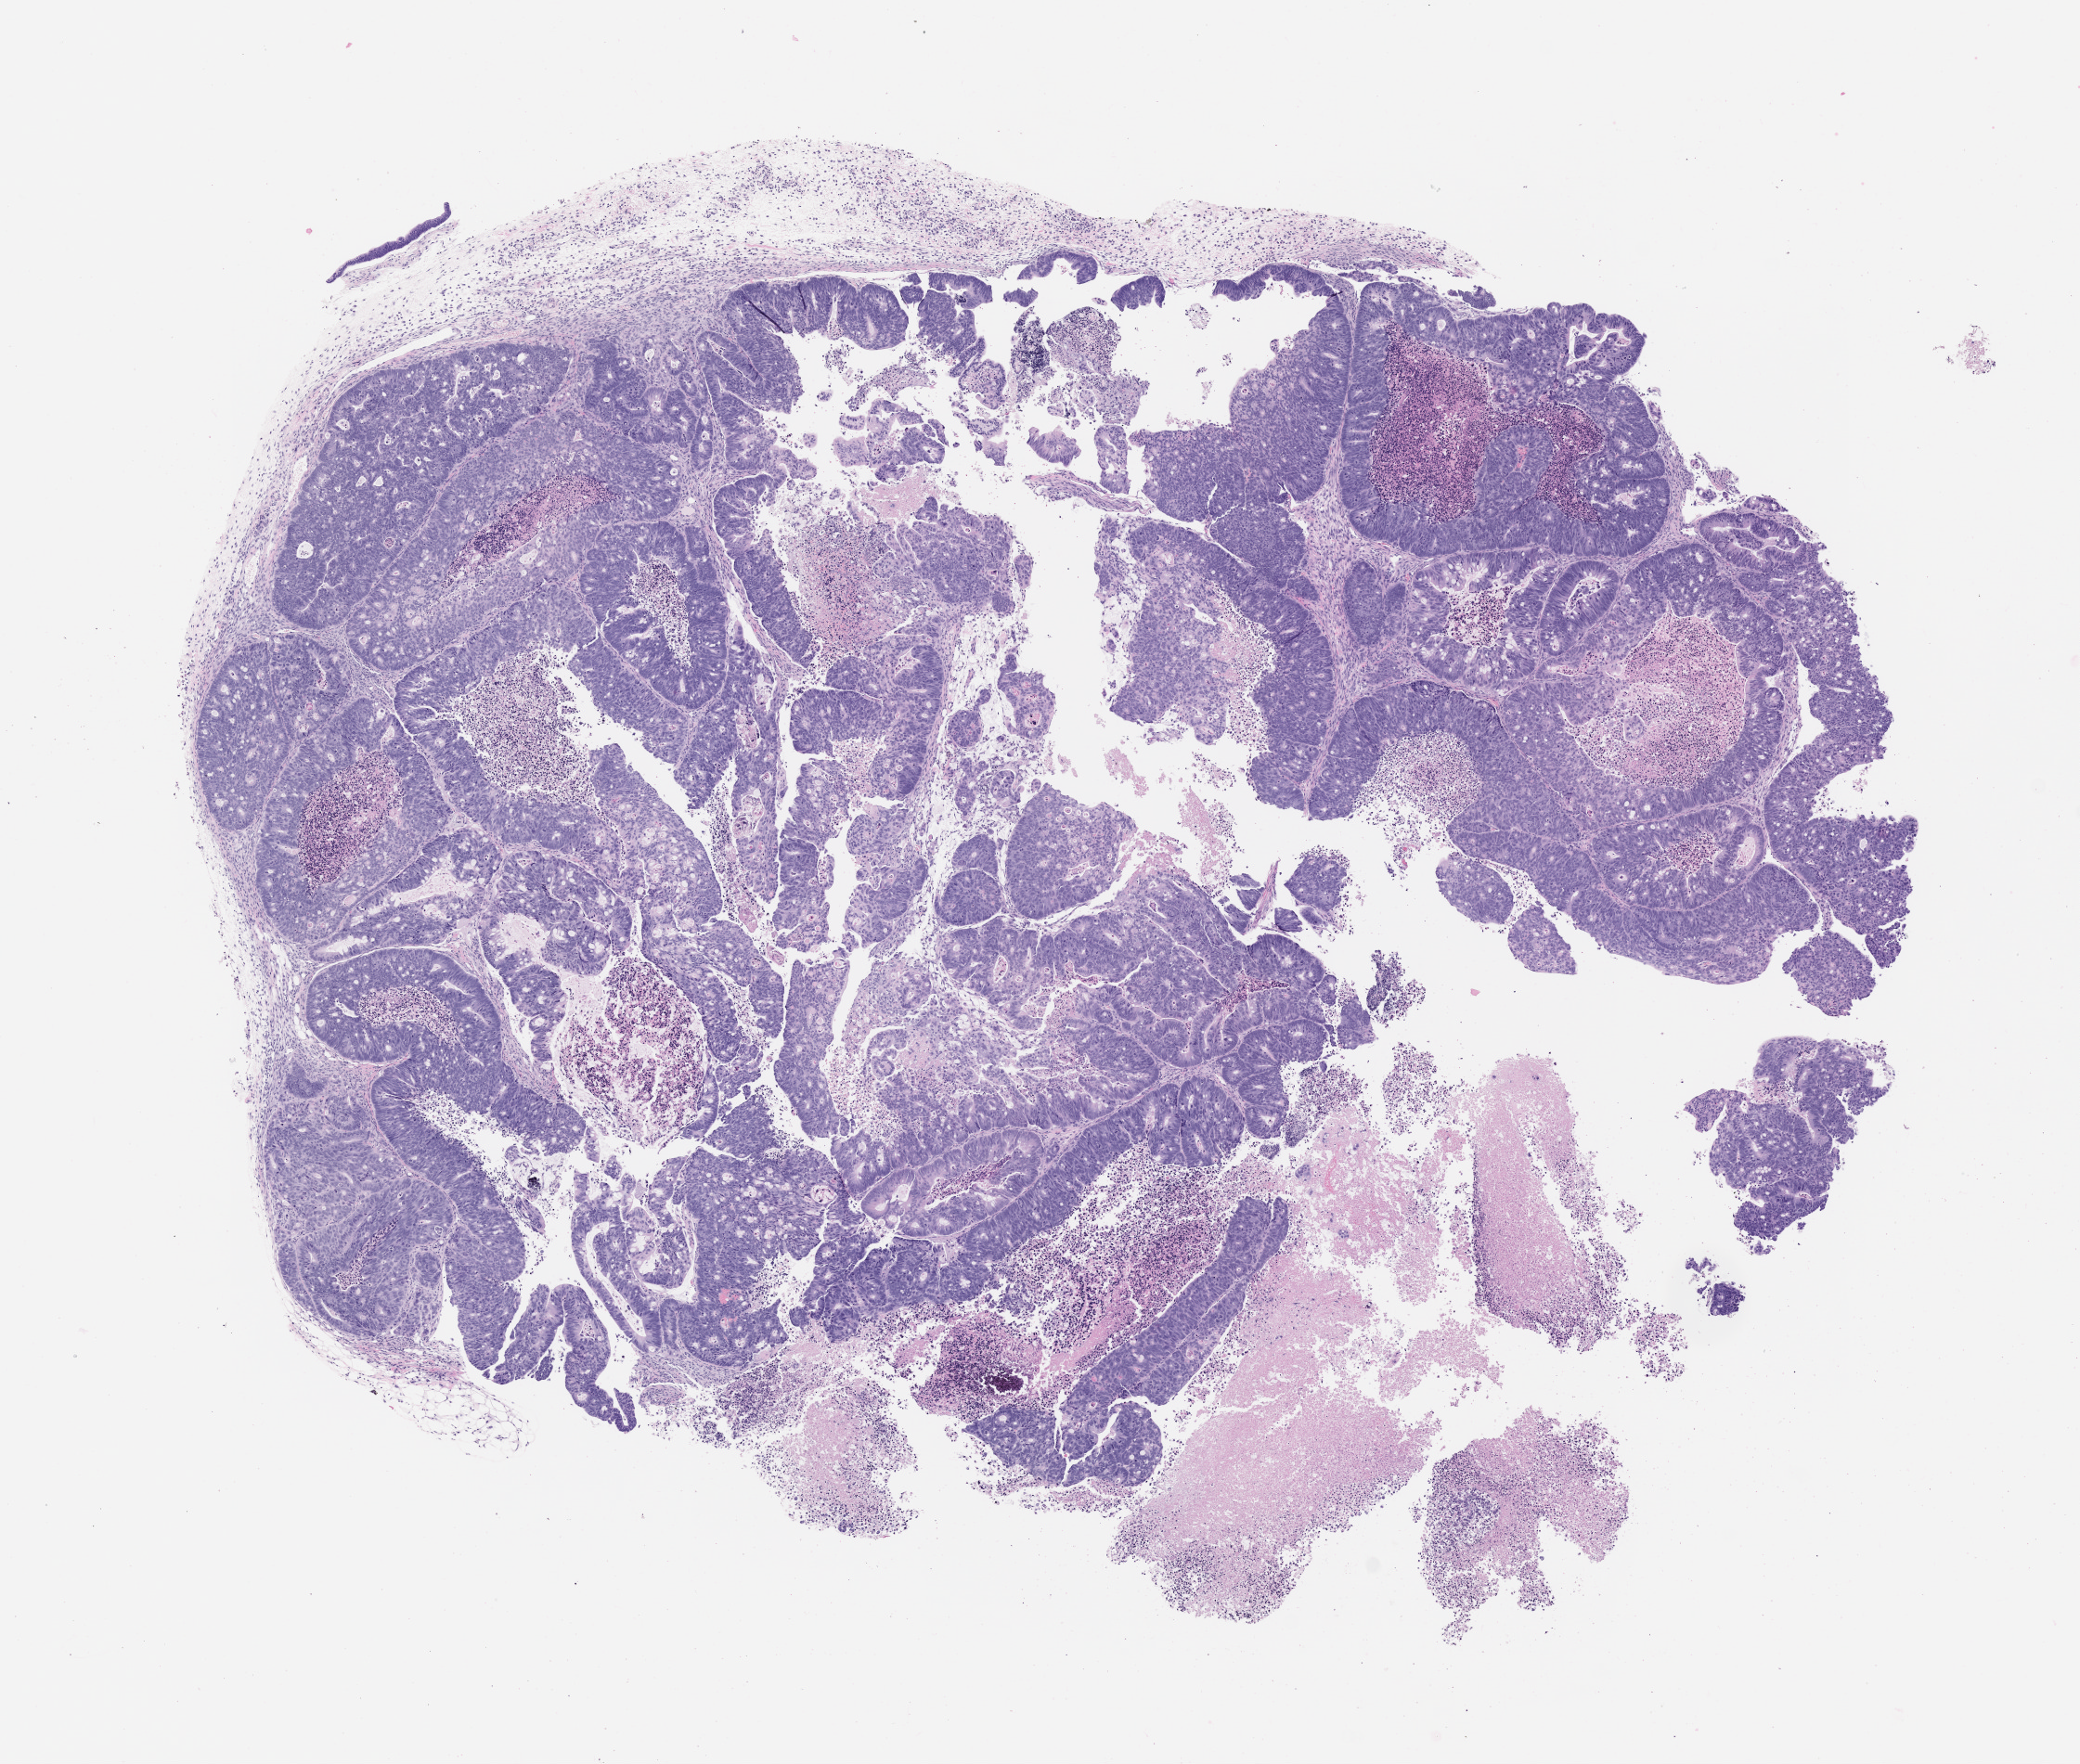
Whole-slide image, H&E: patient-derived xenograft (human tumor grown in a mouse), passage 2, whole scanned area (about 9.0 x 7.6 mm) shown as a low-resolution overview. Formalin-fixed paraffin-embedded section. Originating tumor site category: colon.
Originating patient diagnosis: Colon Adenocarcinoma.